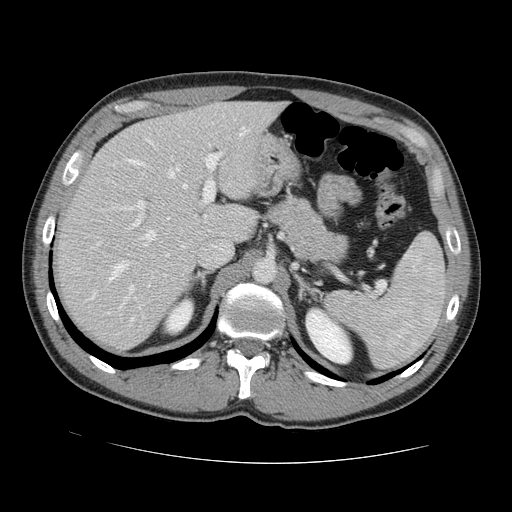
Contrast-enhanced abdominal CT, one axial slice. Slice 90 of 131 in the series (ordered by position). Intravenous contrast given. Soft-tissue window (W 400 / L 40 HU). 2.5 mm slice thickness. 512 × 512 image matrix, field of view 380 × 380 mm. Male patient, age 40 years. Case-level facts recorded for this patient, not image findings: diagnosis: colorectal cancer liver metastases, imaged before liver resection.
Annotated regions visible in this slice (expert manual segmentation):
- hepatic veins: box from (x=90, y=158) to (x=187, y=321) px
- liver: (x=59, y=102)–(x=281, y=349)
- planned liver remnant (the part of the liver to remain after resection): (x=101, y=102)–(x=282, y=242)
- portal vein (with intrahepatic branches): (x=91, y=153)–(x=221, y=314)